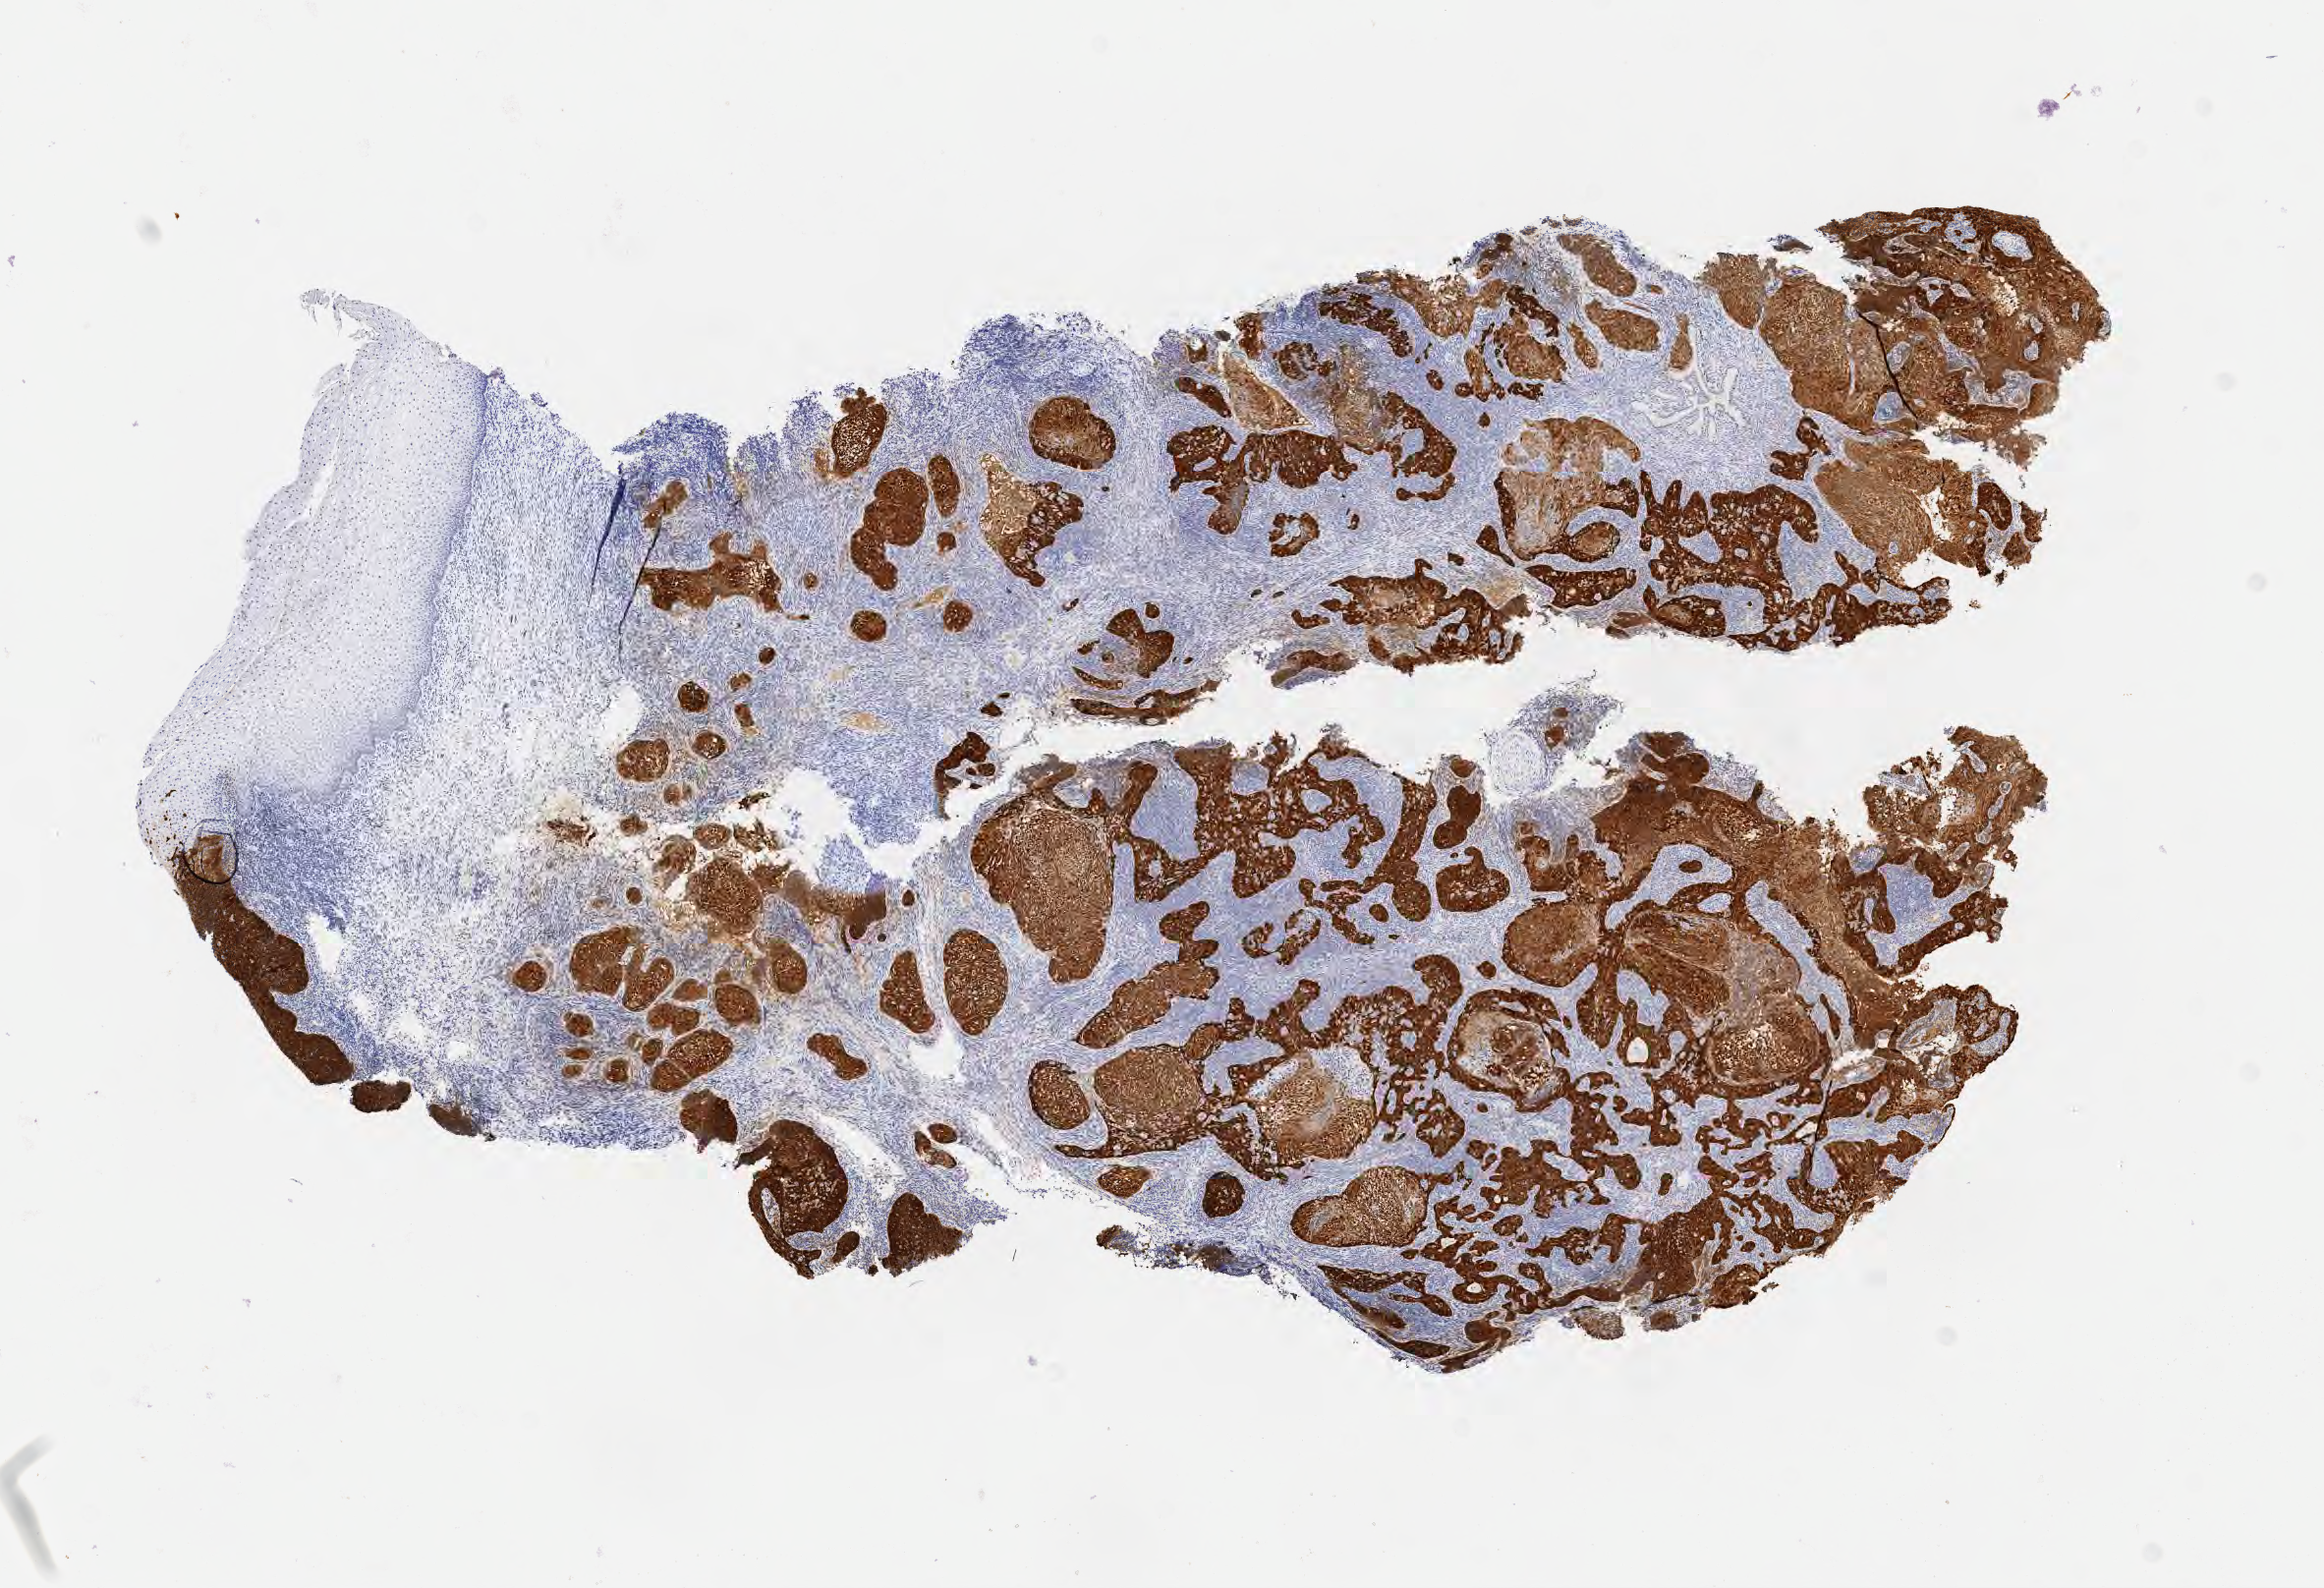
Immunohistochemistry (IHC) whole-slide image stained for p16 (p16INK4a) — whole scanned area (about 9.6 x 6.5 mm) shown as a low-resolution overview. Specimen: tumor tissue. Site: cervix. Patient: female, aged 53.
Diagnosis: Squamous cell carcinoma, large cell, nonkeratinizing, NOS.